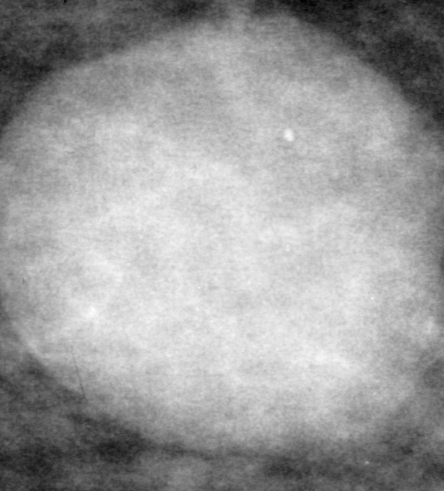
Region of interest cut from a scanned film mammogram (one marked finding); right breast; MLO view; BI-RADS breast density category 2 (scale 1–4).
Finding: mass, shape oval, margins ill defined; BI-RADS assessment category 4; pathology (as recorded): malignant.